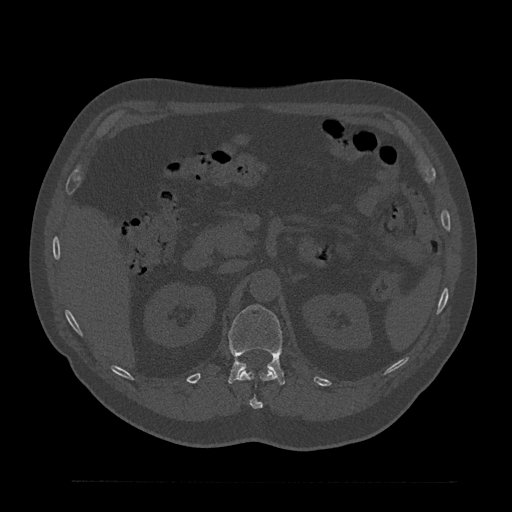
CT including the spine, one axial slice; position 190 of 797 along the scan axis; reconstruction kernel Br40s/3; 120 kVp; bone window (W 1800 / L 400 HU); 0.5 mm slice thickness; 512 × 512 image matrix. Male patient, age 61 years. Case-level facts recorded for this patient, not image findings: primary cancer: prostate.
Structures marked on this image (semi-automatic segmentation, software-assisted and operator-edited):
- L1 vertebra: bounding box (x1, y1, x2, y2) in pixels: (228, 305, 285, 385)
- T12 vertebra: (238, 370, 276, 409)